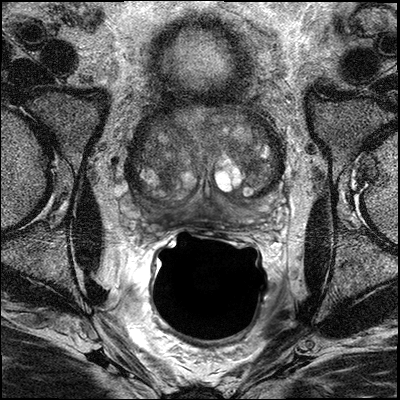
MRI of the prostate; 3 images, each a single mid-volume slice chosen by position (not for content). Treatment context recorded for this patient: No surgery, Casodex, leuprolide and RT.
Image 1: T2-weighted axial slice, series "T2W_TSE_AX", slice 20 of 38, 3 mm slice thickness.
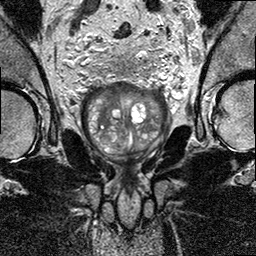
Image 2: T2-weighted coronal slice, series "T2W_TSE_COR", slice 17 of 32, 3 mm slice thickness.
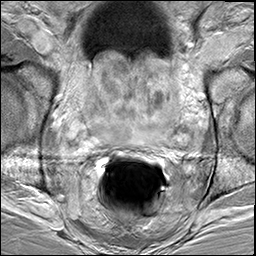
Image 3: DCE (dynamic gadolinium-enhanced) axial slice, slice 21 of 41, dynamic phase 5 of 8, 6 mm slice thickness.
Radiologist's MRI report for this examination:
The prostate has a maximal lateral diameter of 6.5 cm, a maximal craniocaudal diameter of 7.5cm with prominent median lobe protruding into bladder neck; and a maximal AP diameter of 5.6 cm resulting in an estimated gland volume of 141 cc. The zonal anatomy is preserved, however there is a markedly enlarged central gland with a very large median lobe protruding into the bladder neck, consistent with marked BPH. There are several small irregular areas of T2-hyperintensity with suspicious contrast enhancement. in the posterior lateral left and right peripheral zone at 4-5 o'clock and 7-8 o'clock, respectively, in the mid and upper third of the prostate. Capsular infiltration is possible on both sides. Minimal extracapsular extension is more likely on the left side (left posterior lateral peripheral zone; mid third at 5 o'clock). In addition suspicious area of enhancement in the midthird of the prostate in the right central gland and a small area in the left aspect of the median lobe. No evidence for involvement of the neurovascular bundle on either side. There is minimal enhancement at the seminal vesicles based on both sides, however, manifest seminal vesicles infiltration is not visualized. No evidence of involvement of urinary bladder neck and rectal wall. (The lobulated enhancement of the bladder neck on CT, was caused by the prominent median lobe of the prostate). No suspiciously enlarged obturator lymph nodes. There is a 10 x 8 mm rounded left iliac lymph node just above level of the upper seminal vesicles and a second 10 x 6 mm lymph node (both just posterior to the left iliac vein. The lymph nodes do not show a fatty hilum. Multiplanar reconstructions, subtraction images, and CAD analysis of the dynamic series for assessment of the kinetic information facilitated the interpretation of the exam. IMPRESSION: 1) Multifocal possible bilateral prostate cancer with capsular infiltration and possible minimal extracapsular extension more likely on the left (ECE possible left posterior lateral). 2) No involvement of the neurovascular bundle on either side. 3) No manifest infiltration of the seminal vesicles. Beginning infiltration of the seminal vesicle basis is possible. 4) No involvement of the bladder neck. 5) Two adjacent 10 mm left iliac lymph nodes without fatty hilum posterior/dorsal to the left iliac vein just above the level of the upper aspect of the seminal vesicles) 6) Very large prostate (141 cc) due to marked BPH and large median lobe protruding into the bladder neck.

Prostate biopsy pathology (as recorded):
PROSTATE BIOPSIES A. PROSTATE (RIGHT PZ), NEEDLE CORE BIOPSY PROSTATIC TISSUE. NO TUMOR IDENTIFIED. B. PROSTATE (RIGHT PZ/TZ), NEDDLE CORE BIOPSY: PROSTATIC TISSUE. NO TUMOR IDENTIFIED. C. PROSTATE (RIGHT APEX), NEEDLE CORE BIOPSY PROSTATIC TISSUE. NO TUMOR IDENTIFIED. D. PROSTATE (LEFT PZ), NEEDLE CORE BIOPSY PROSTATIC ADENOCARCINOMA, GLEASON SCORE 3+4 = 7/10, INVOLVING THREE (3) OF FIVE (5) CORES, APPROXIMATELY 20% OF TISSUE EXAMINED. PERINEURAL INVASION IS IDENTIFIED. E. PROSTATE (LEFT PZ/TZ), NEEDLE CORE BIOPSY: PROSTATIC ADENOCARCINOMA, GLEASON SCORE 3+4 = 7/10, INVOLVING ONE (1) OF THREE(3) CORES, LESS THAN 5% OF TISSUE EXAMINED. F. PROSTATE (LEFT APEX), NEEDLE CORE BIOPSY: PROSTATIC TISSUE. NO TUMOR IDENTIFIED.